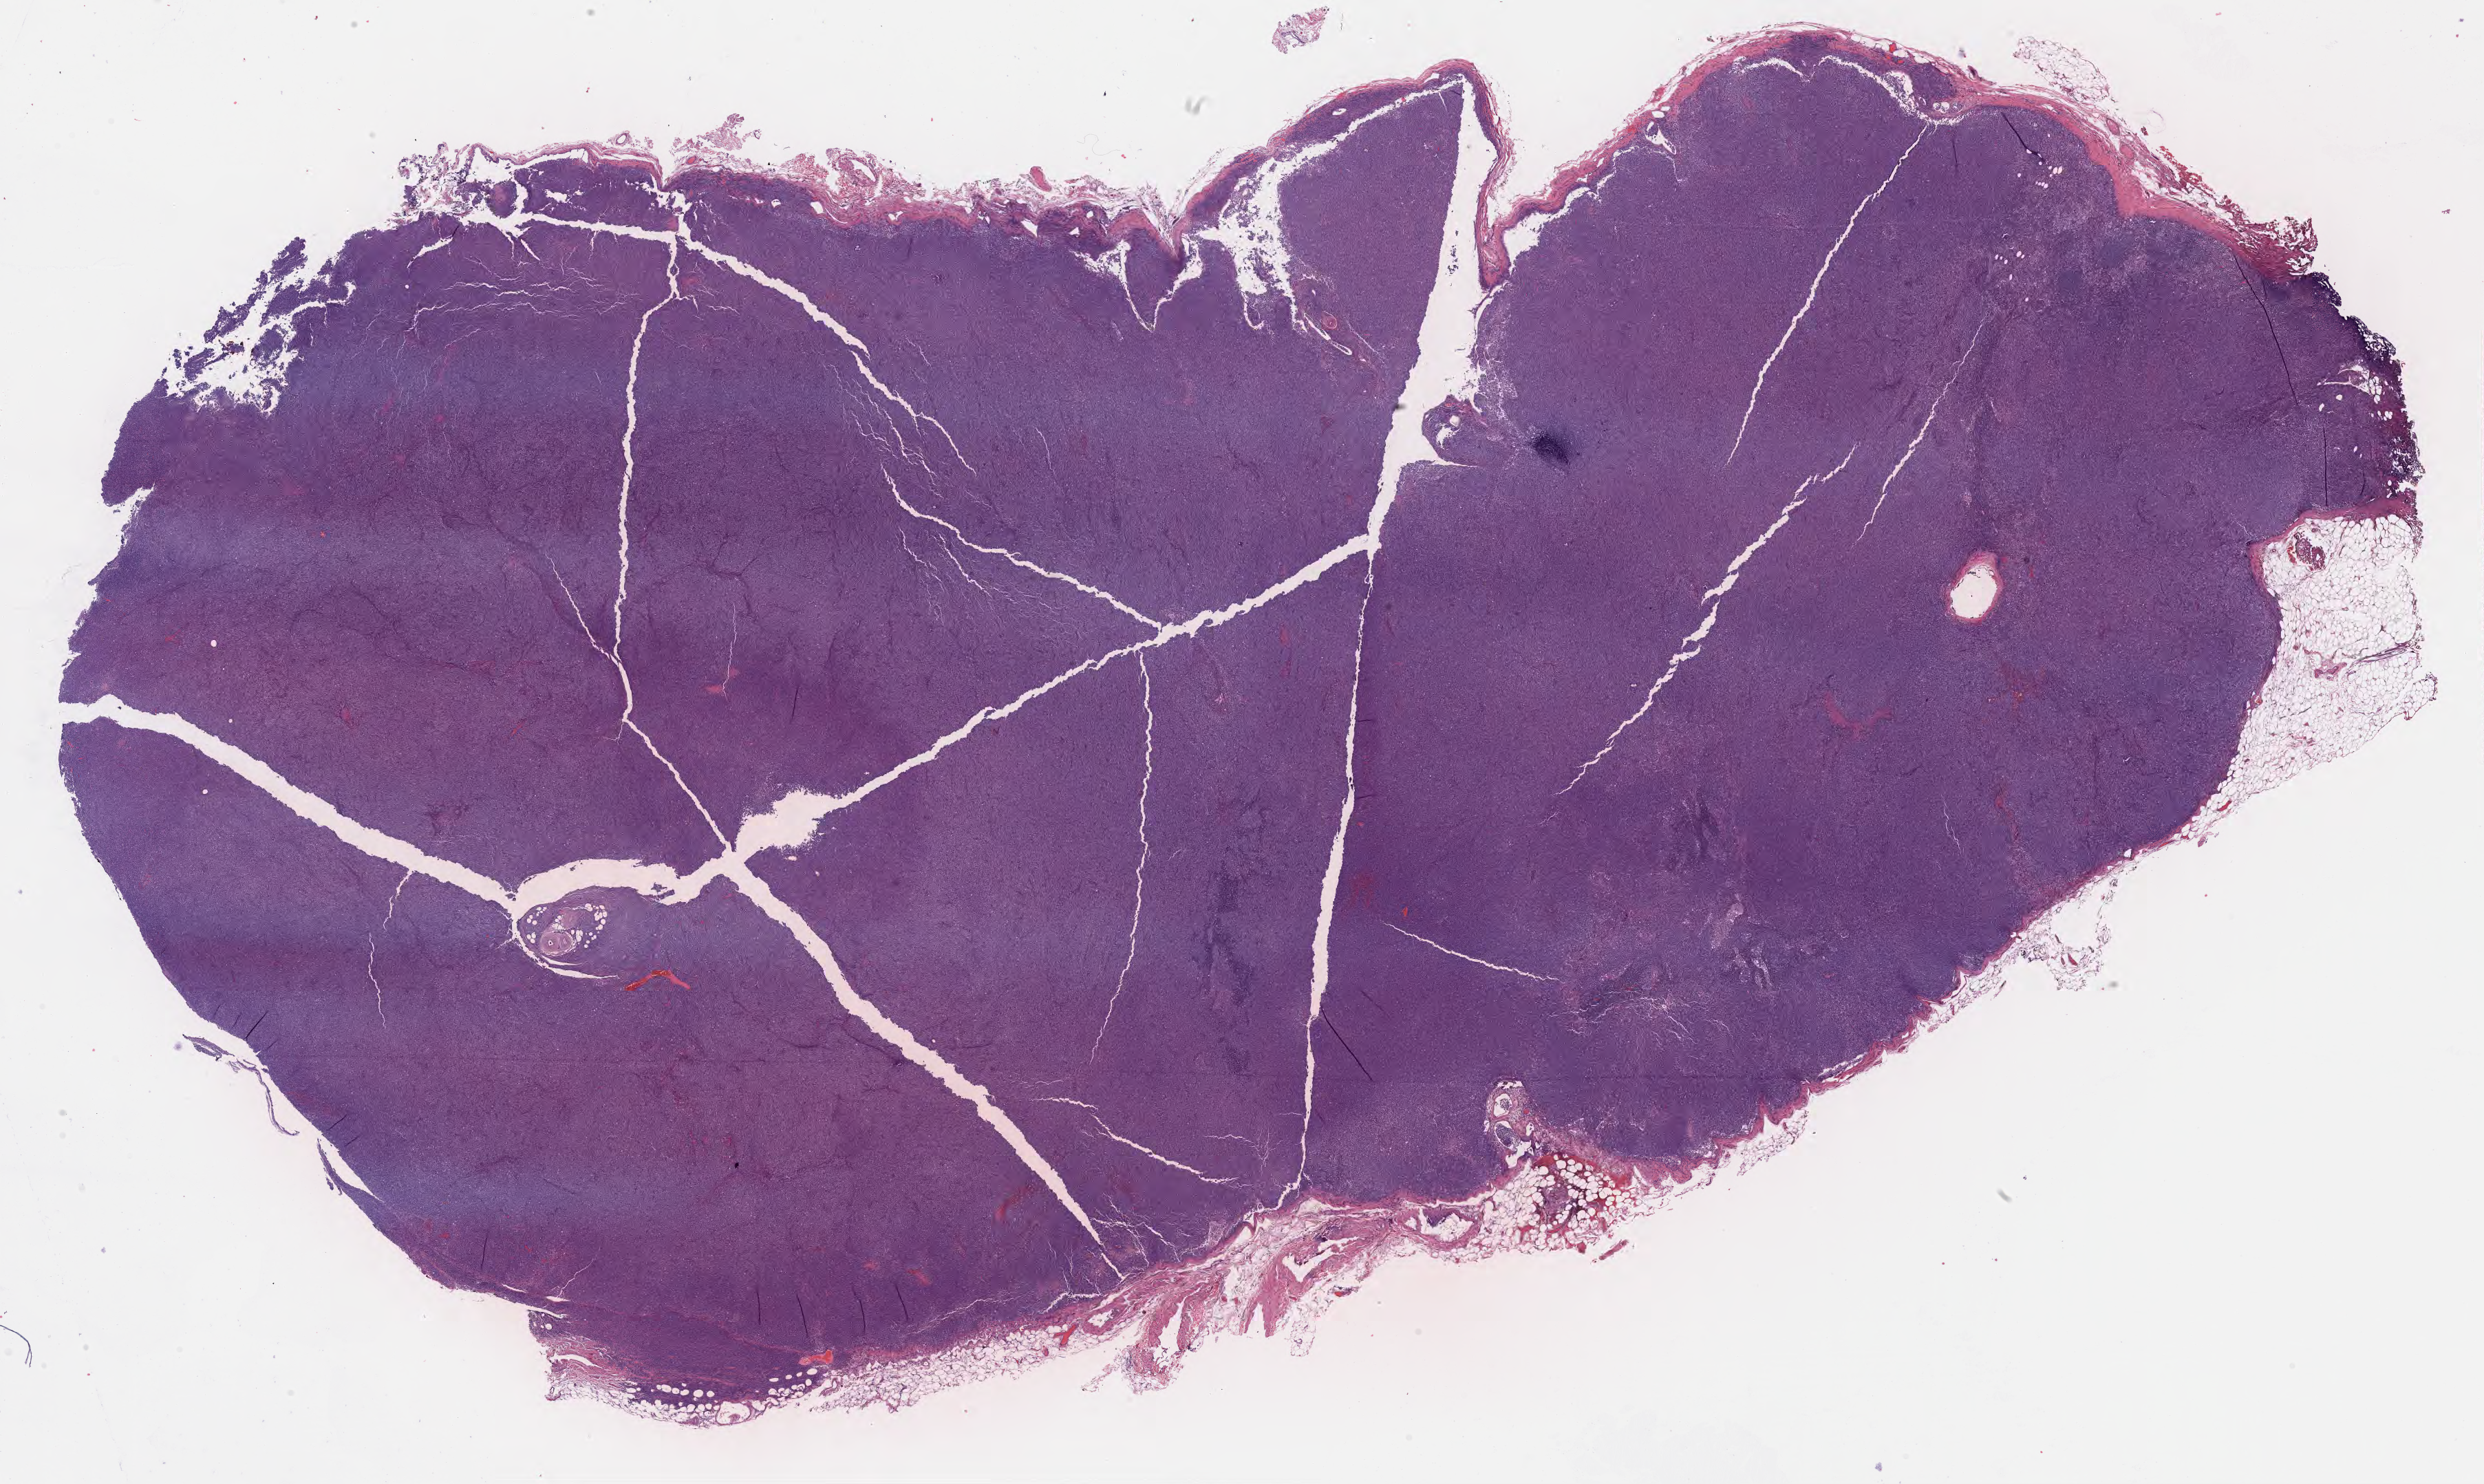
Hematoxylin and eosin (H&E) whole-slide image, a low-resolution overview of the entire scanned area, about 29.2 x 17.4 mm, tumor tissue. Patient: male, 69 years old.
* diagnosis: Diffuse large B-cell lymphoma, NOS